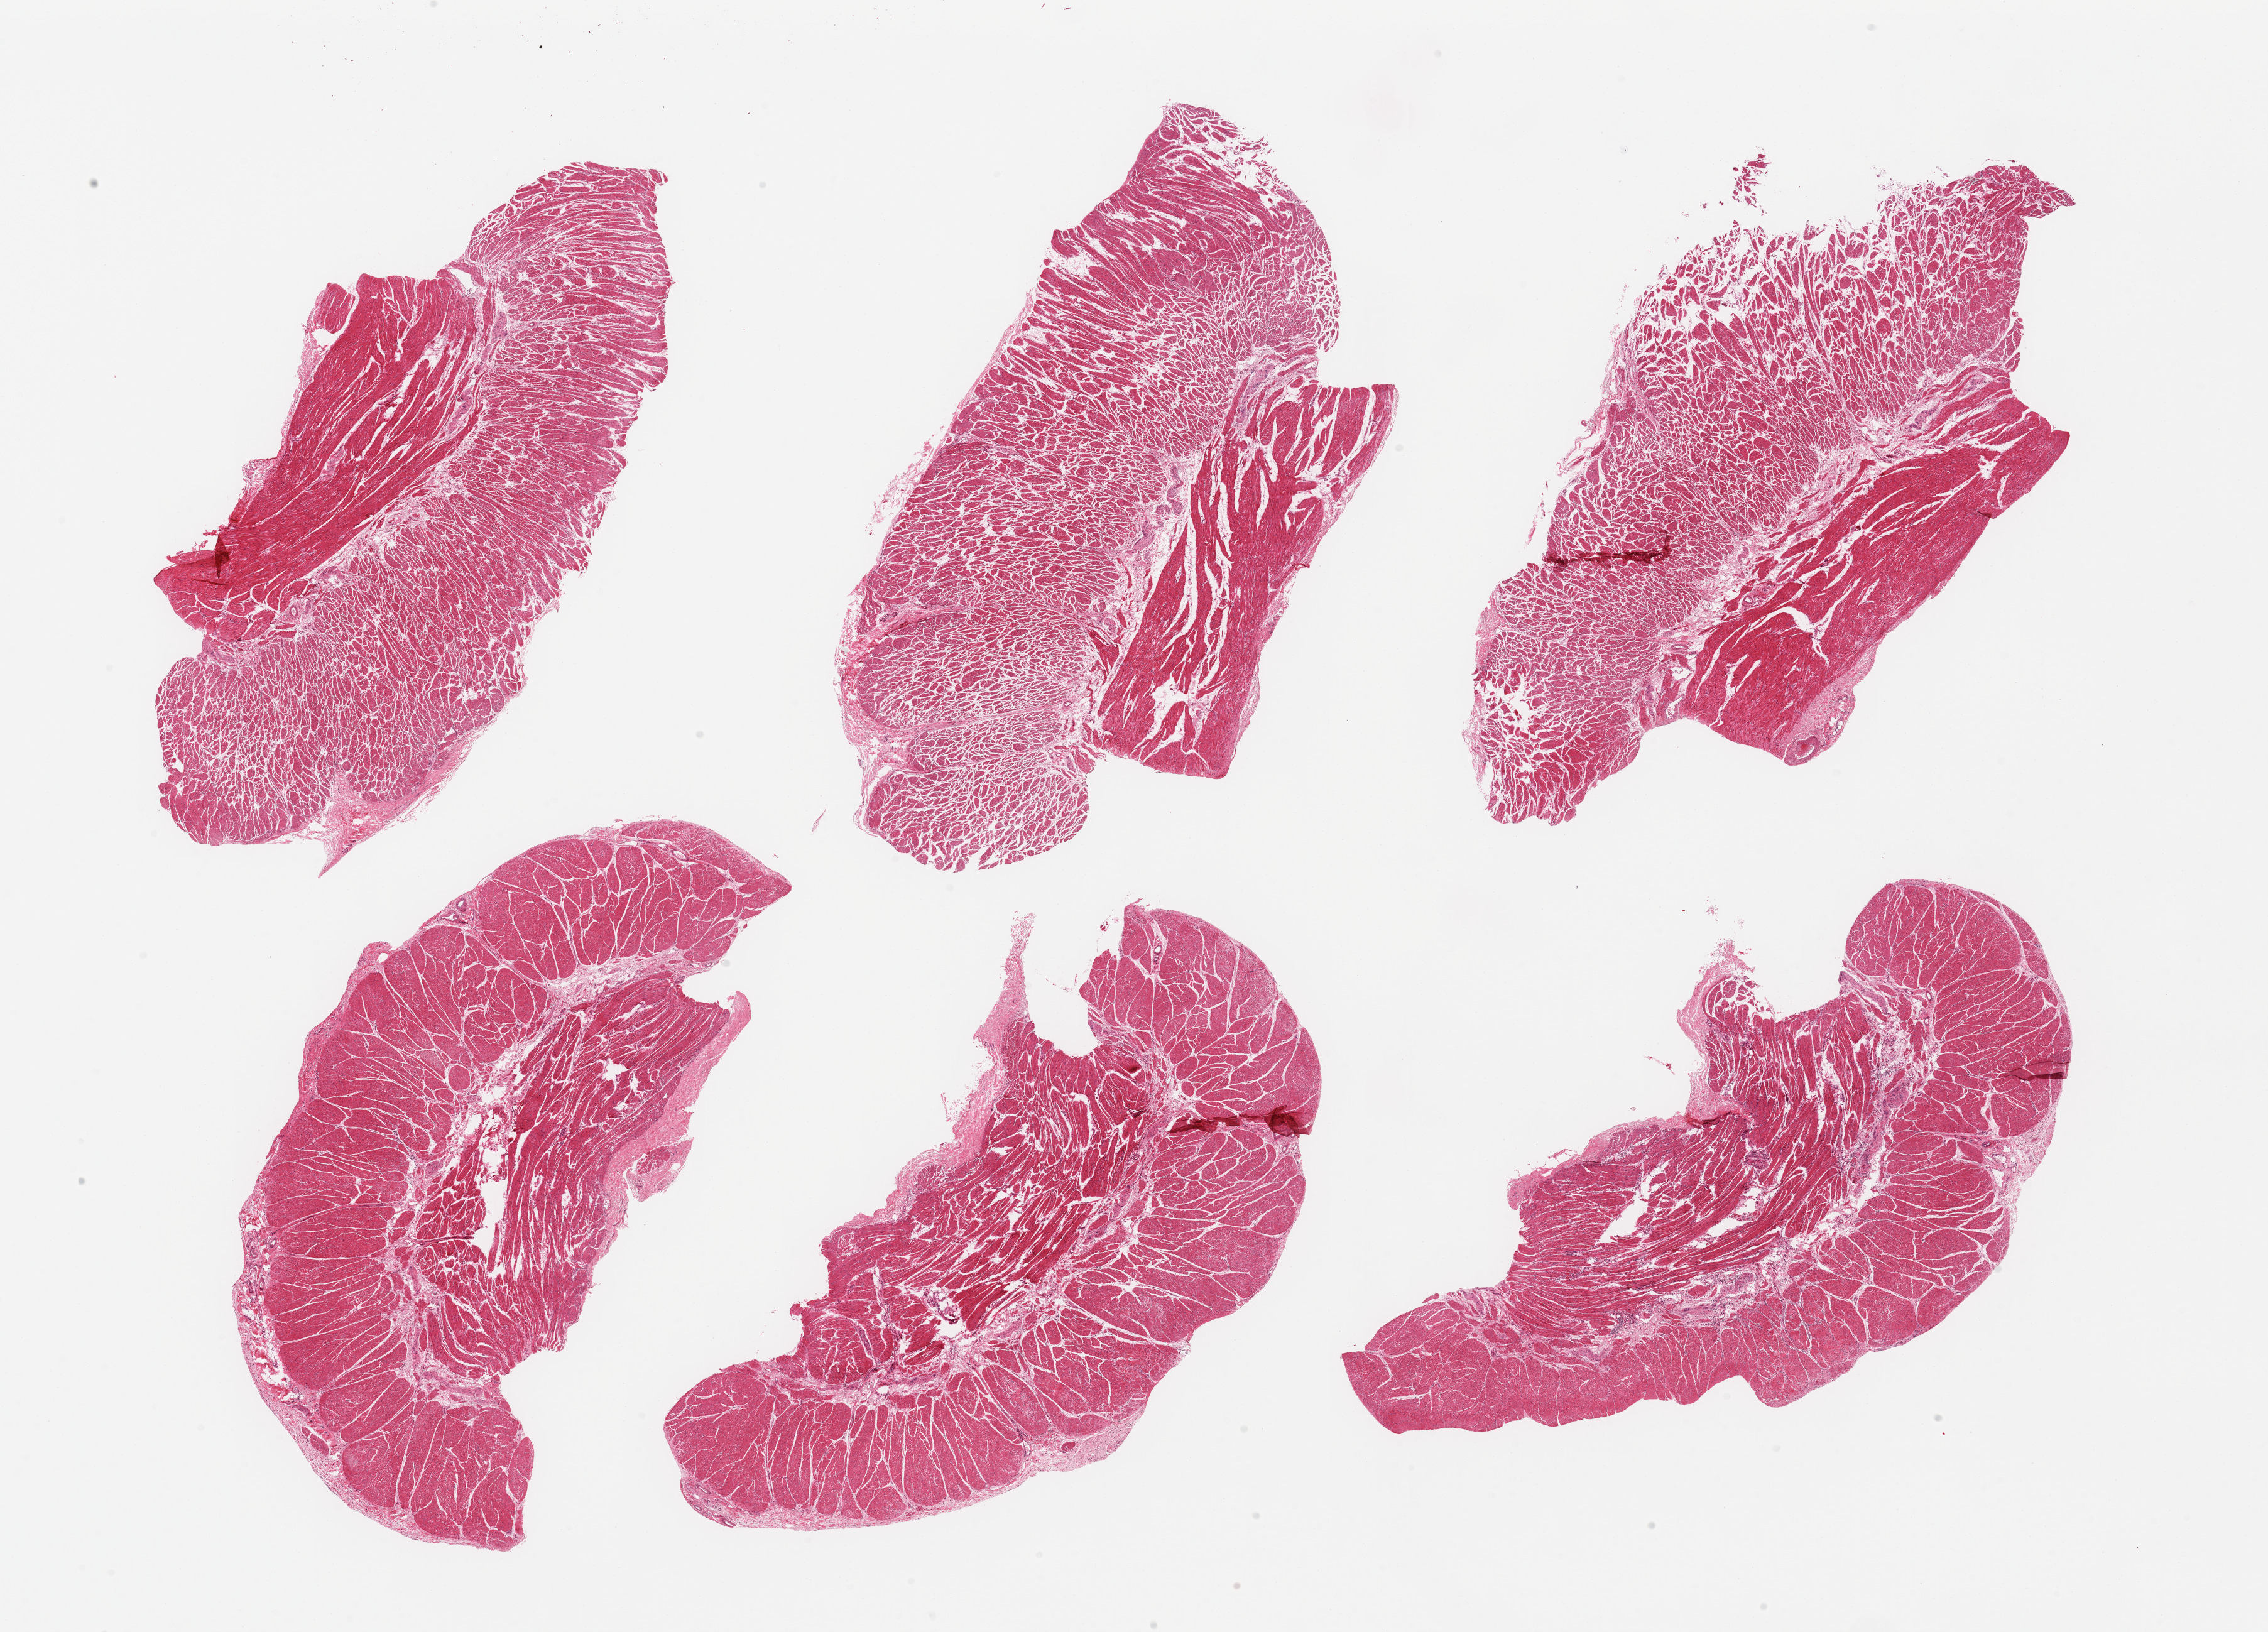
Digitized hematoxylin and eosin (H&E)-stained section, whole scanned area (about 28.5 x 20.5 mm, acquisition: 20x scan) shown as a low-resolution overview, PAXgene-fixed paraffin-embedded (PFPE) section, sampled site (target tissue): esophageal muscle, donor tissue sample. Female donor.
Reviewer comment on this tissue sample: 6 pieces; target muscularis.